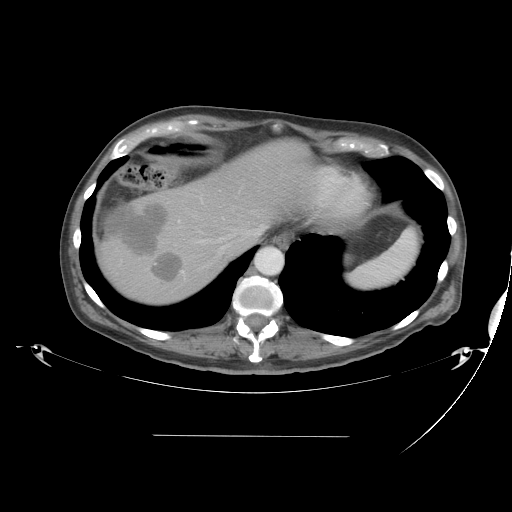
Contrast-enhanced abdominal CT, one axial slice; slice 36 of 48 in the series (ordered by position); reconstruction kernel STANDARD; 120 kVp; intravenous contrast given; soft-tissue window (W 400 / L 40 HU); 512 × 512 image matrix. Male patient, age 65 years. From the clinical record (not read from this slice): diagnosis: colorectal cancer liver metastases, imaged before liver resection; multiple liver metastases: yes; largest metastasis: 11 cm.
Outlined on this slice (outlined manually by an expert reader):
- hepatic veins: bounding box (x1, y1, x2, y2) in pixels: (189, 214, 266, 268)
- liver: (96, 140, 318, 308)
- planned liver remnant (the part of the liver to remain after resection): (184, 140, 317, 235)
- portal vein (with intrahepatic branches): (177, 194, 225, 229)
- liver metastasis: (152, 254, 182, 279)
- liver metastasis: (105, 205, 167, 258)